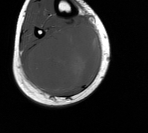
MRI of an extremity soft-tissue mass, one axial slice; slice 48 of 76 in the series (ordered by position); MR volume resampled by the dataset authors to the PET/CT grid (not the native acquisition matrix); 3.27 mm slice thickness; 148 × 133 image matrix, field of view 145 × 130 mm. Male patient. Case-level facts recorded for this patient, not image findings: histological type: liposarcoma - round cell; grade: high; site of the primary tumour: right calf.
Structures marked on this image (expert contour drawn on MRI and transferred to this co-registered scan by the dataset authors):
- gross tumour volume (mass): bounding box <24,23,100,93> (left, top, right, bottom; pixels)